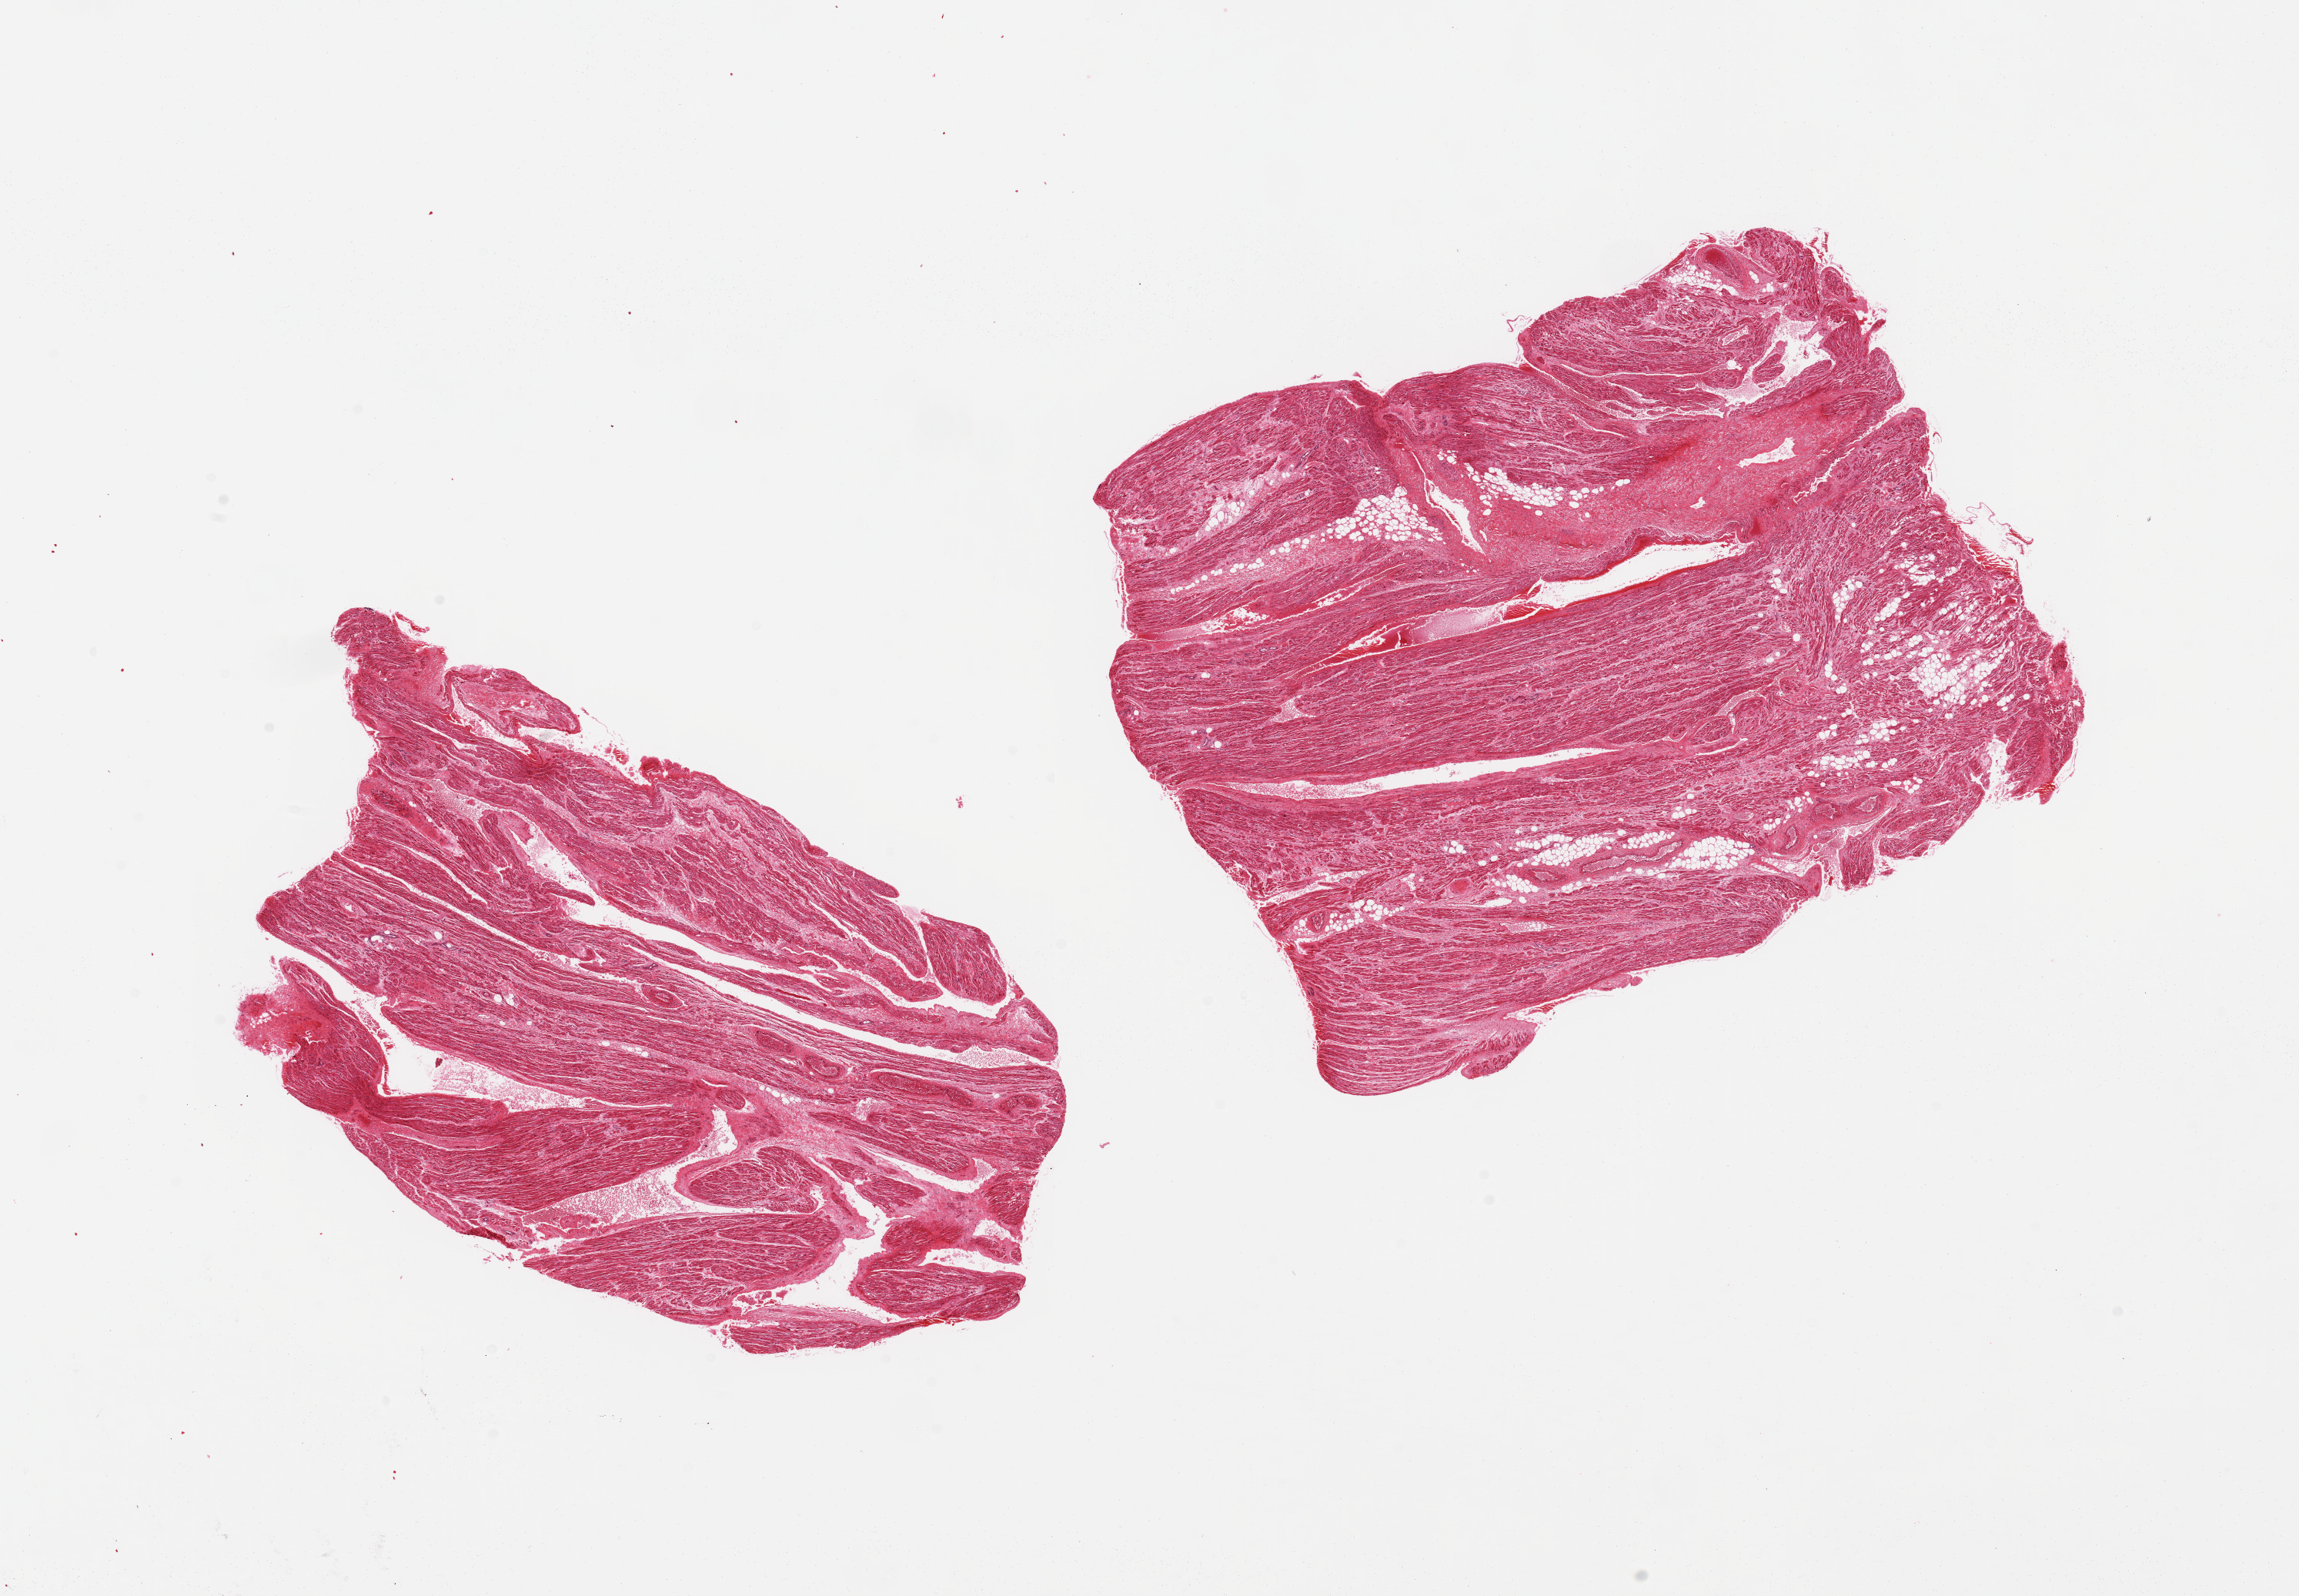
Digitized hematoxylin and eosin (H&E)-stained section, shown as a low-resolution overview of the whole scanned area (about 23.6 x 16.4 mm, acquisition: 20x scan), PAXgene-fixed, paraffin-embedded tissue, target tissue: auricular appendage, tissue donor sample. Donor sex: male.
* reviewer comment on this tissue sample: 2 pieces; 10% internal fat in 1 piece